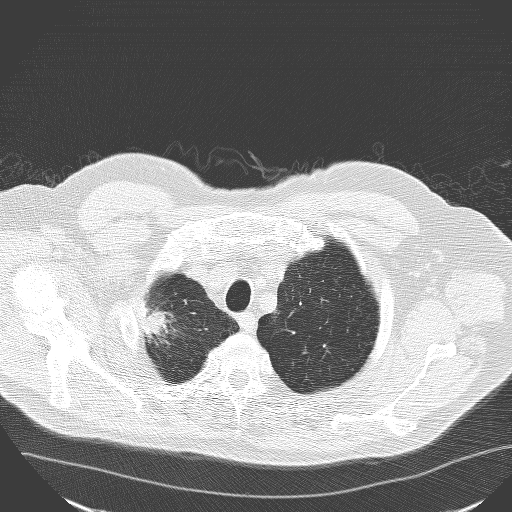
Low-dose screening chest CT, one axial slice. Position 143 of 160 along the scan axis. 120 kVp. Lung window (W 1500 / L -600 HU). 3.2 mm slice thickness. 512 × 512 image matrix, field of view 400 × 400 mm.
Structures marked on this image (expert manual segmentation):
- lesion 1 (tumor, upper lobe of right lung): bounding box (x1, y1, x2, y2) in pixels: (143, 308, 166, 337)